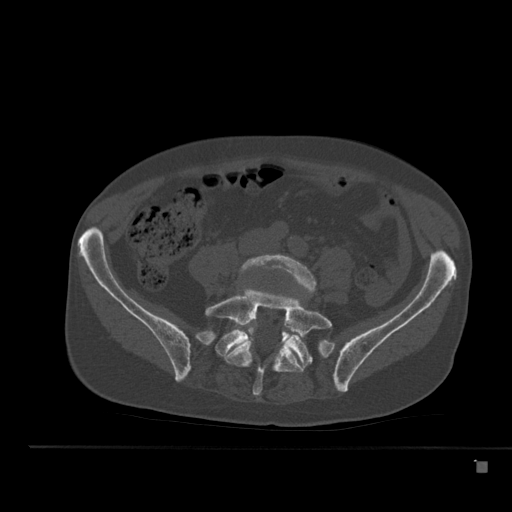
CT including the spine, one axial slice; position 126 of 517 along the scan axis; 120 kVp; bone window (W 1800 / L 400 HU); 512 × 512 image matrix, field of view 408 × 408 mm. Male patient, age 70 years. From the clinical record (not read from this slice): primary cancer: renal; vertebrae with lytic lesions (as recorded): T4, T6, T10, T12, L3, L4, L5.
Annotated regions visible in this slice (semi-automatically segmented with operator editing):
- L4 vertebra: bounding box <239,254,316,329> (left, top, right, bottom; pixels)
- L5 vertebra: <205,289,332,396>